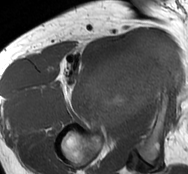
MRI of an extremity soft-tissue mass, one axial slice. Position 62 of 93 along the scan axis. MR volume resampled by the dataset authors to the PET/CT grid (not the native acquisition matrix). 3.27 mm slice thickness. 188 × 174 image matrix, field of view 184 × 170 mm. Male patient. Case-level facts recorded for this patient, not image findings: histological type: undifferentiated - pleiomorphic; grade: high; site of the primary tumour: right thigh.
Outlined on this slice (expert contour drawn on MRI and transferred to this co-registered scan by the dataset authors):
- gross tumour volume including surrounding oedema: bounding box (x1, y1, x2, y2) in pixels: (84, 31, 181, 129)
- gross tumour volume (mass): (84, 33, 181, 129)